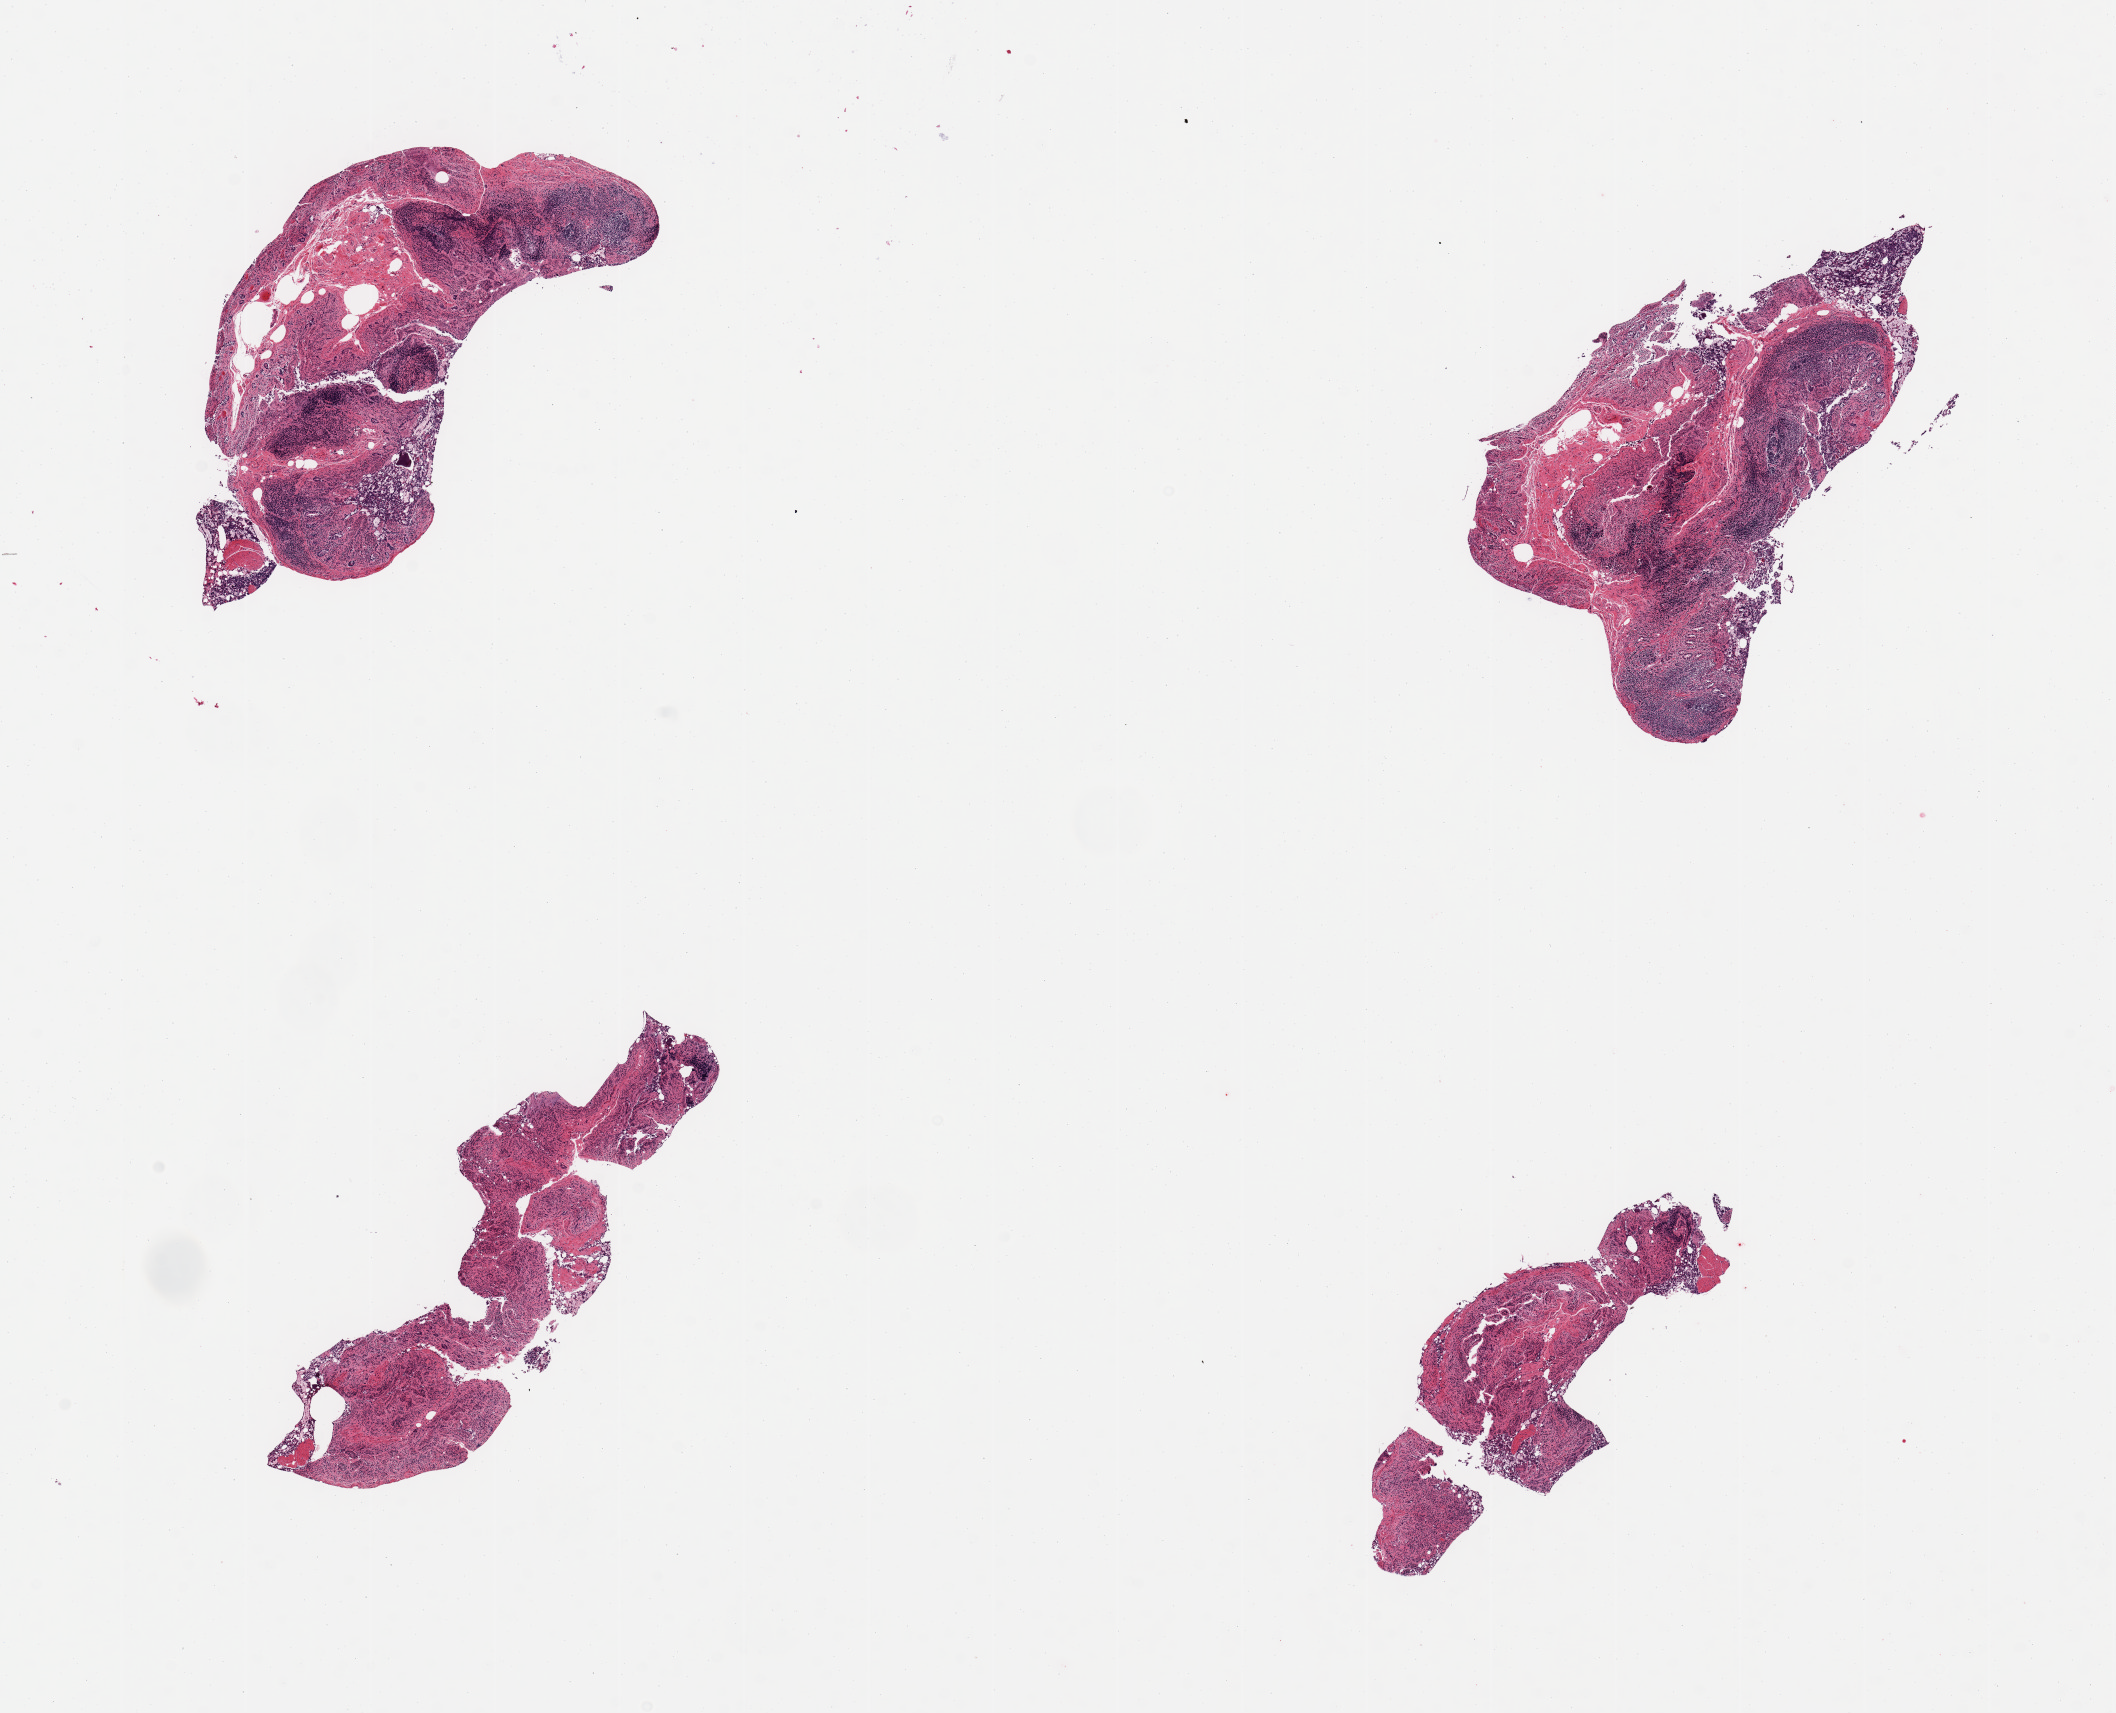
Whole-slide image, hematoxylin and eosin (H&E) stain, low-resolution overview of the scanned area, about 16.7 x 13.5 mm, PAXgene-fixed paraffin-embedded (PFPE) section, target tissue: ileum, tissue donor sample. Donor sex: male.
Reviewer comment on this tissue sample: 4 pieces, autolyzed glandular elements; target lymphoid aggregates are ~30% of remainder.